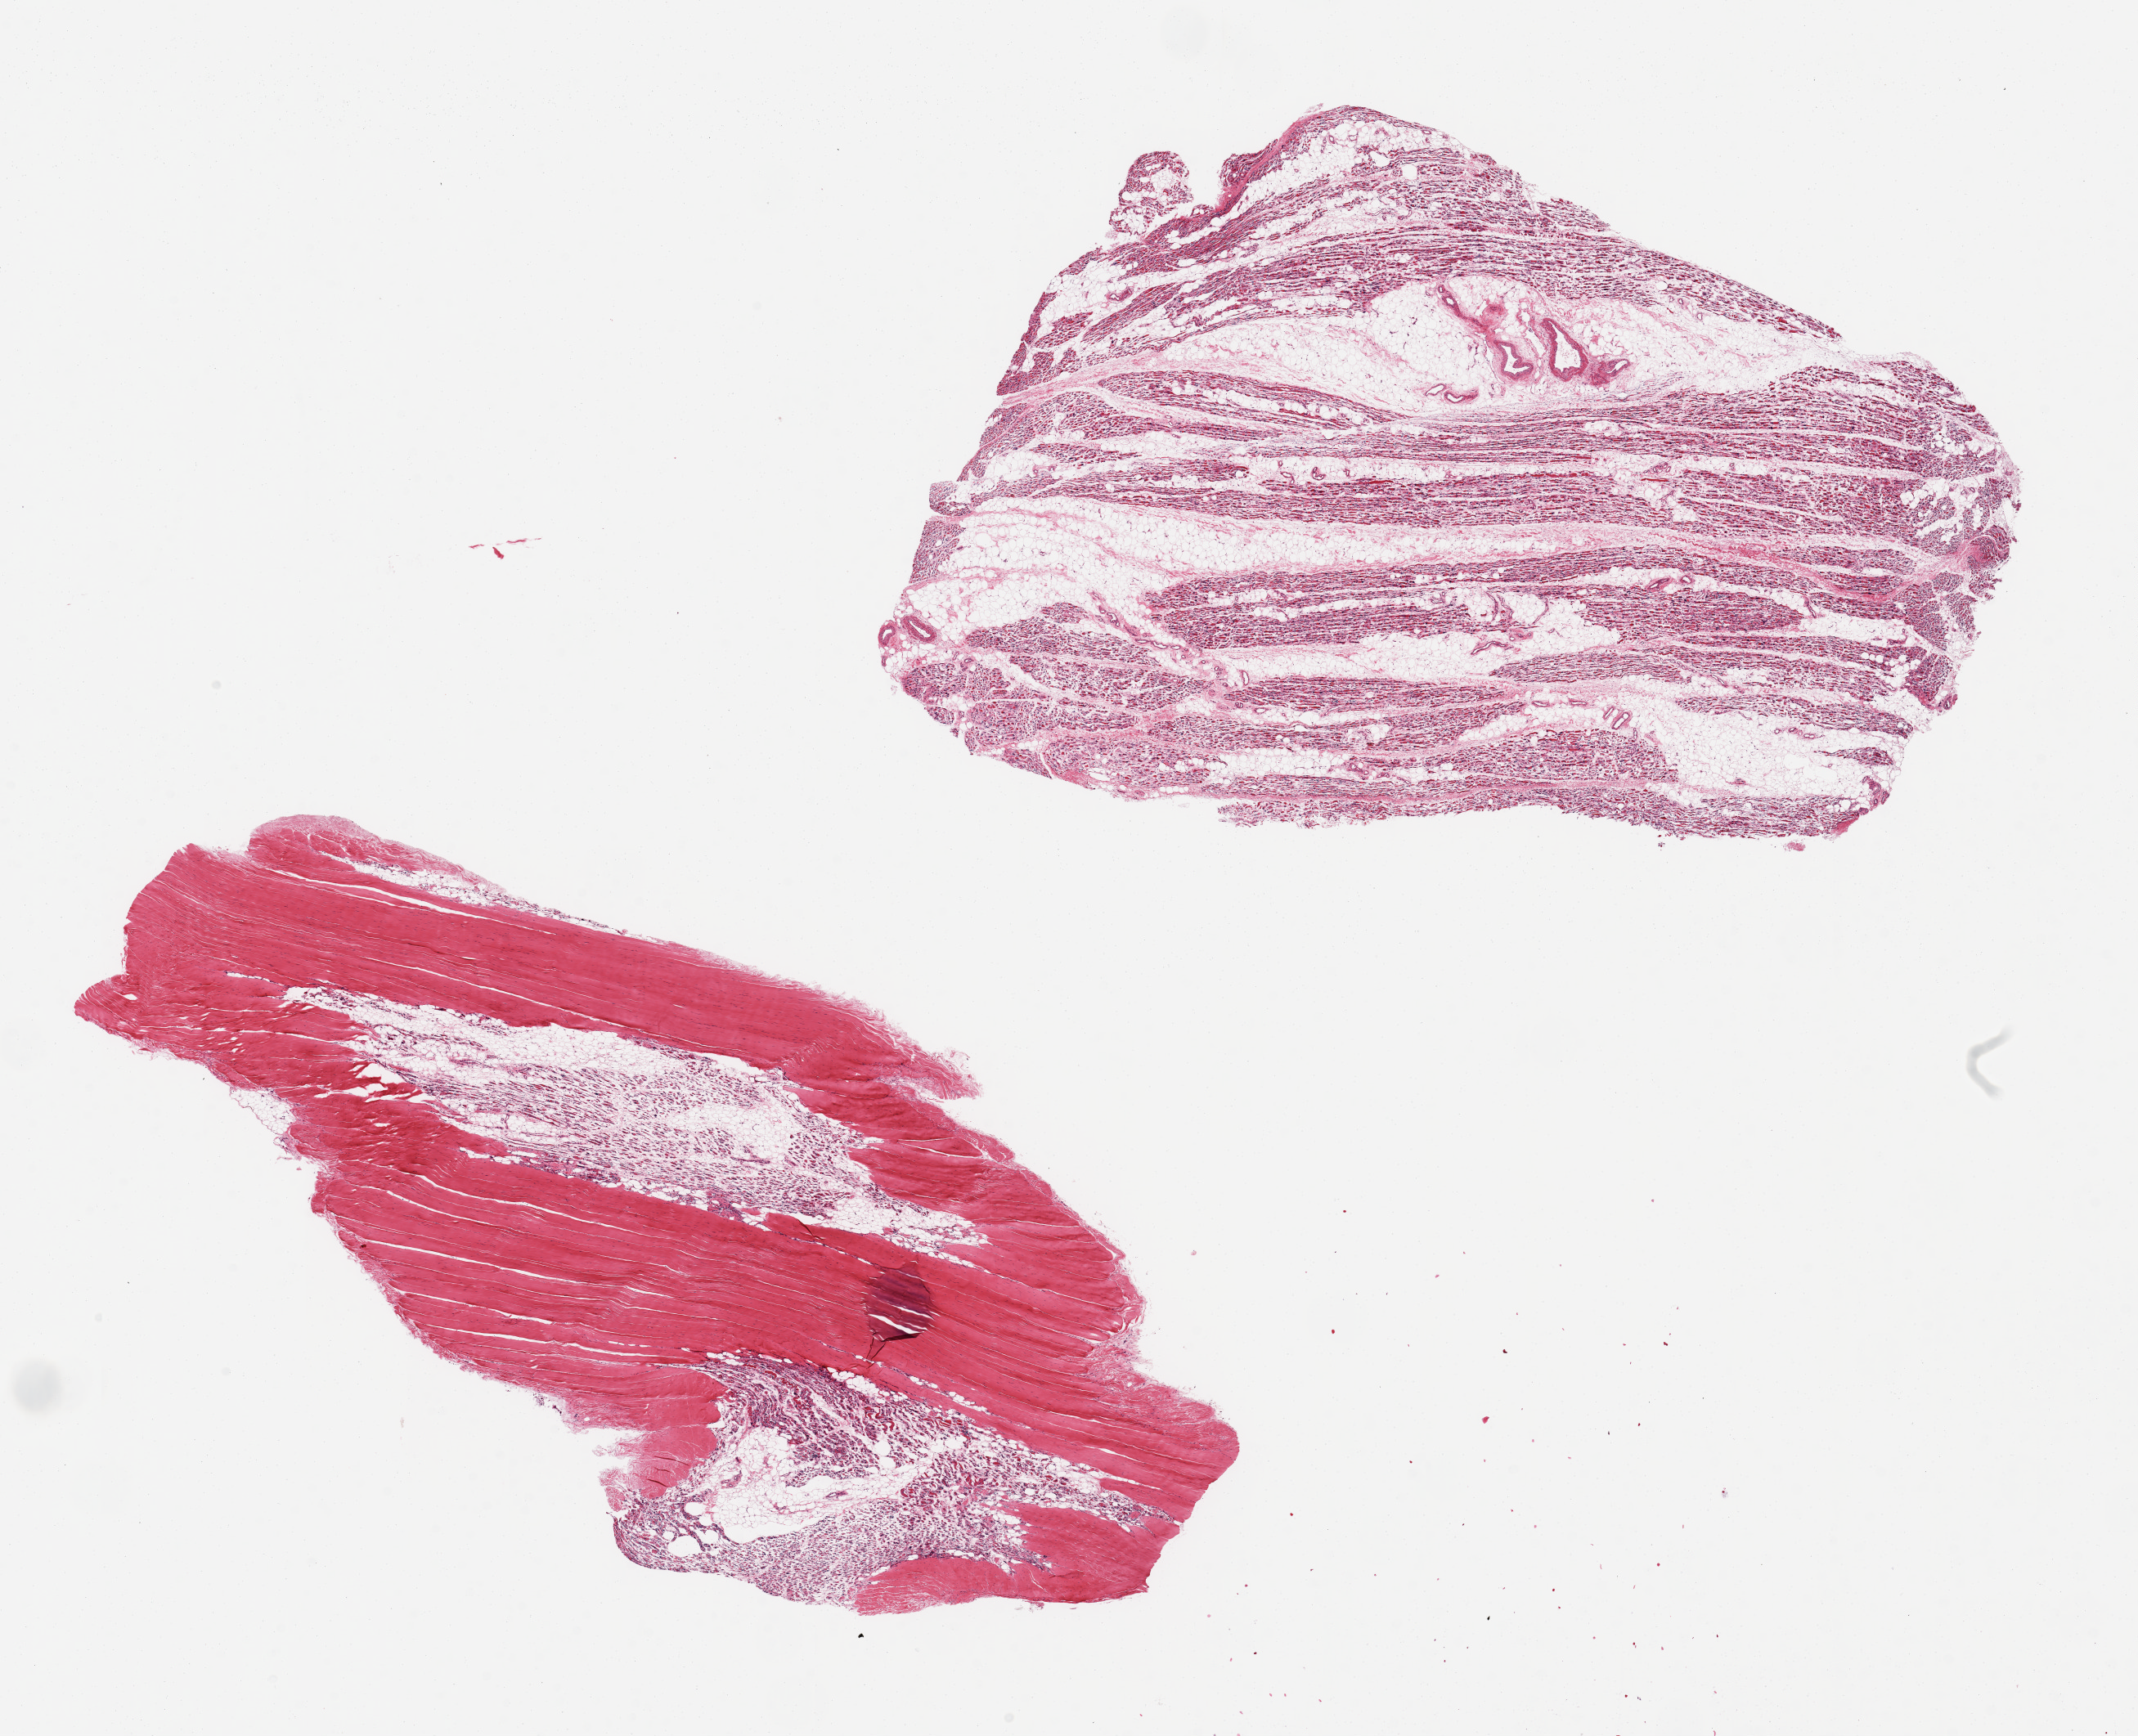
H&E whole-slide image, brightfield, low-resolution overview of the scanned area, about 20.7 x 16.8 mm (from a 20x scan); PAXgene-fixed, paraffin-embedded tissue; section of skeletal muscle (target tissue); donor tissue sample. Donor: female.
• pathologist's review note for this sample: 2 pieces, abnormally degenerated/atrophic muscle in one; the other largely tendion